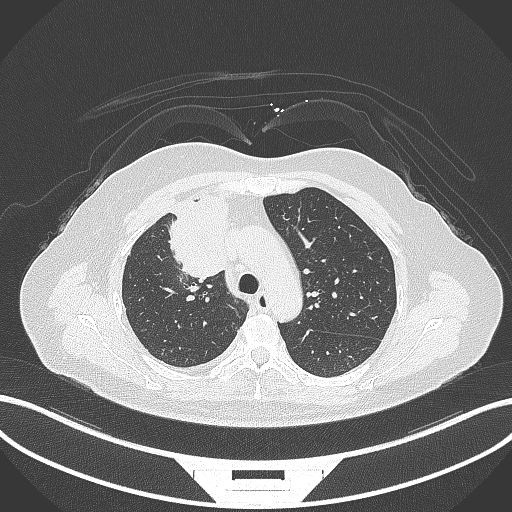
Chest CT, one axial slice. Position 210 of 305 along the scan axis. Reconstruction kernel B70f. 120 kVp. Lung window (W 1500 / L -600 HU). 512 × 512 image matrix, field of view 400 × 400 mm. Patient: female, 52 years. From the clinical record (not read from this slice): clinical TNM (as recorded): T3 N1 M1.
Outlined on this slice (bounding box drawn by a radiologist):
- lung tumour (recorded histology: adenocarcinoma): box from (x=164, y=190) to (x=239, y=282) px